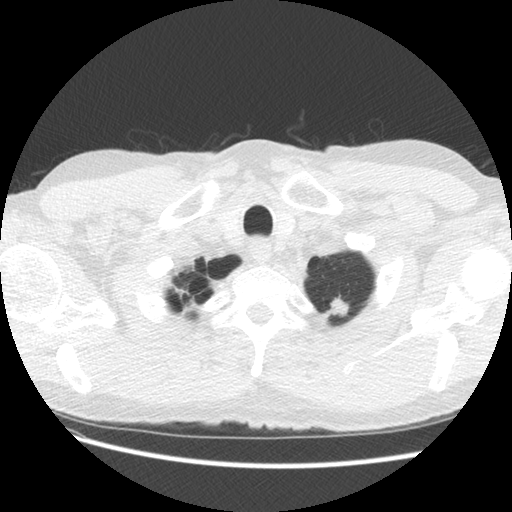
Axial slice from a low-dose chest CT screening exam, second annual screen, lung window (W 1500 / L -600 HU), 2.5 mm slice thickness, 140 kVp, slice 119 of 131 in the series. Male participant, aged 63 years at enrolment.
Expert-annotated lung lesion, bounding box [x1, y1, x2, y2] px = [318, 282, 362, 320]. The screening reader recorded 2 non-calcified nodules or masses ≥4 mm on this exam (left upper lobe, right lower lobe); which of them this box marks is not recorded. Lung cancer was diagnosed 104 days after this screen: adenocarcinoma, NOS, left upper lobe, moderately differentiated (G2), stage IB (AJCC 6th edition), 14 mm at pathology.